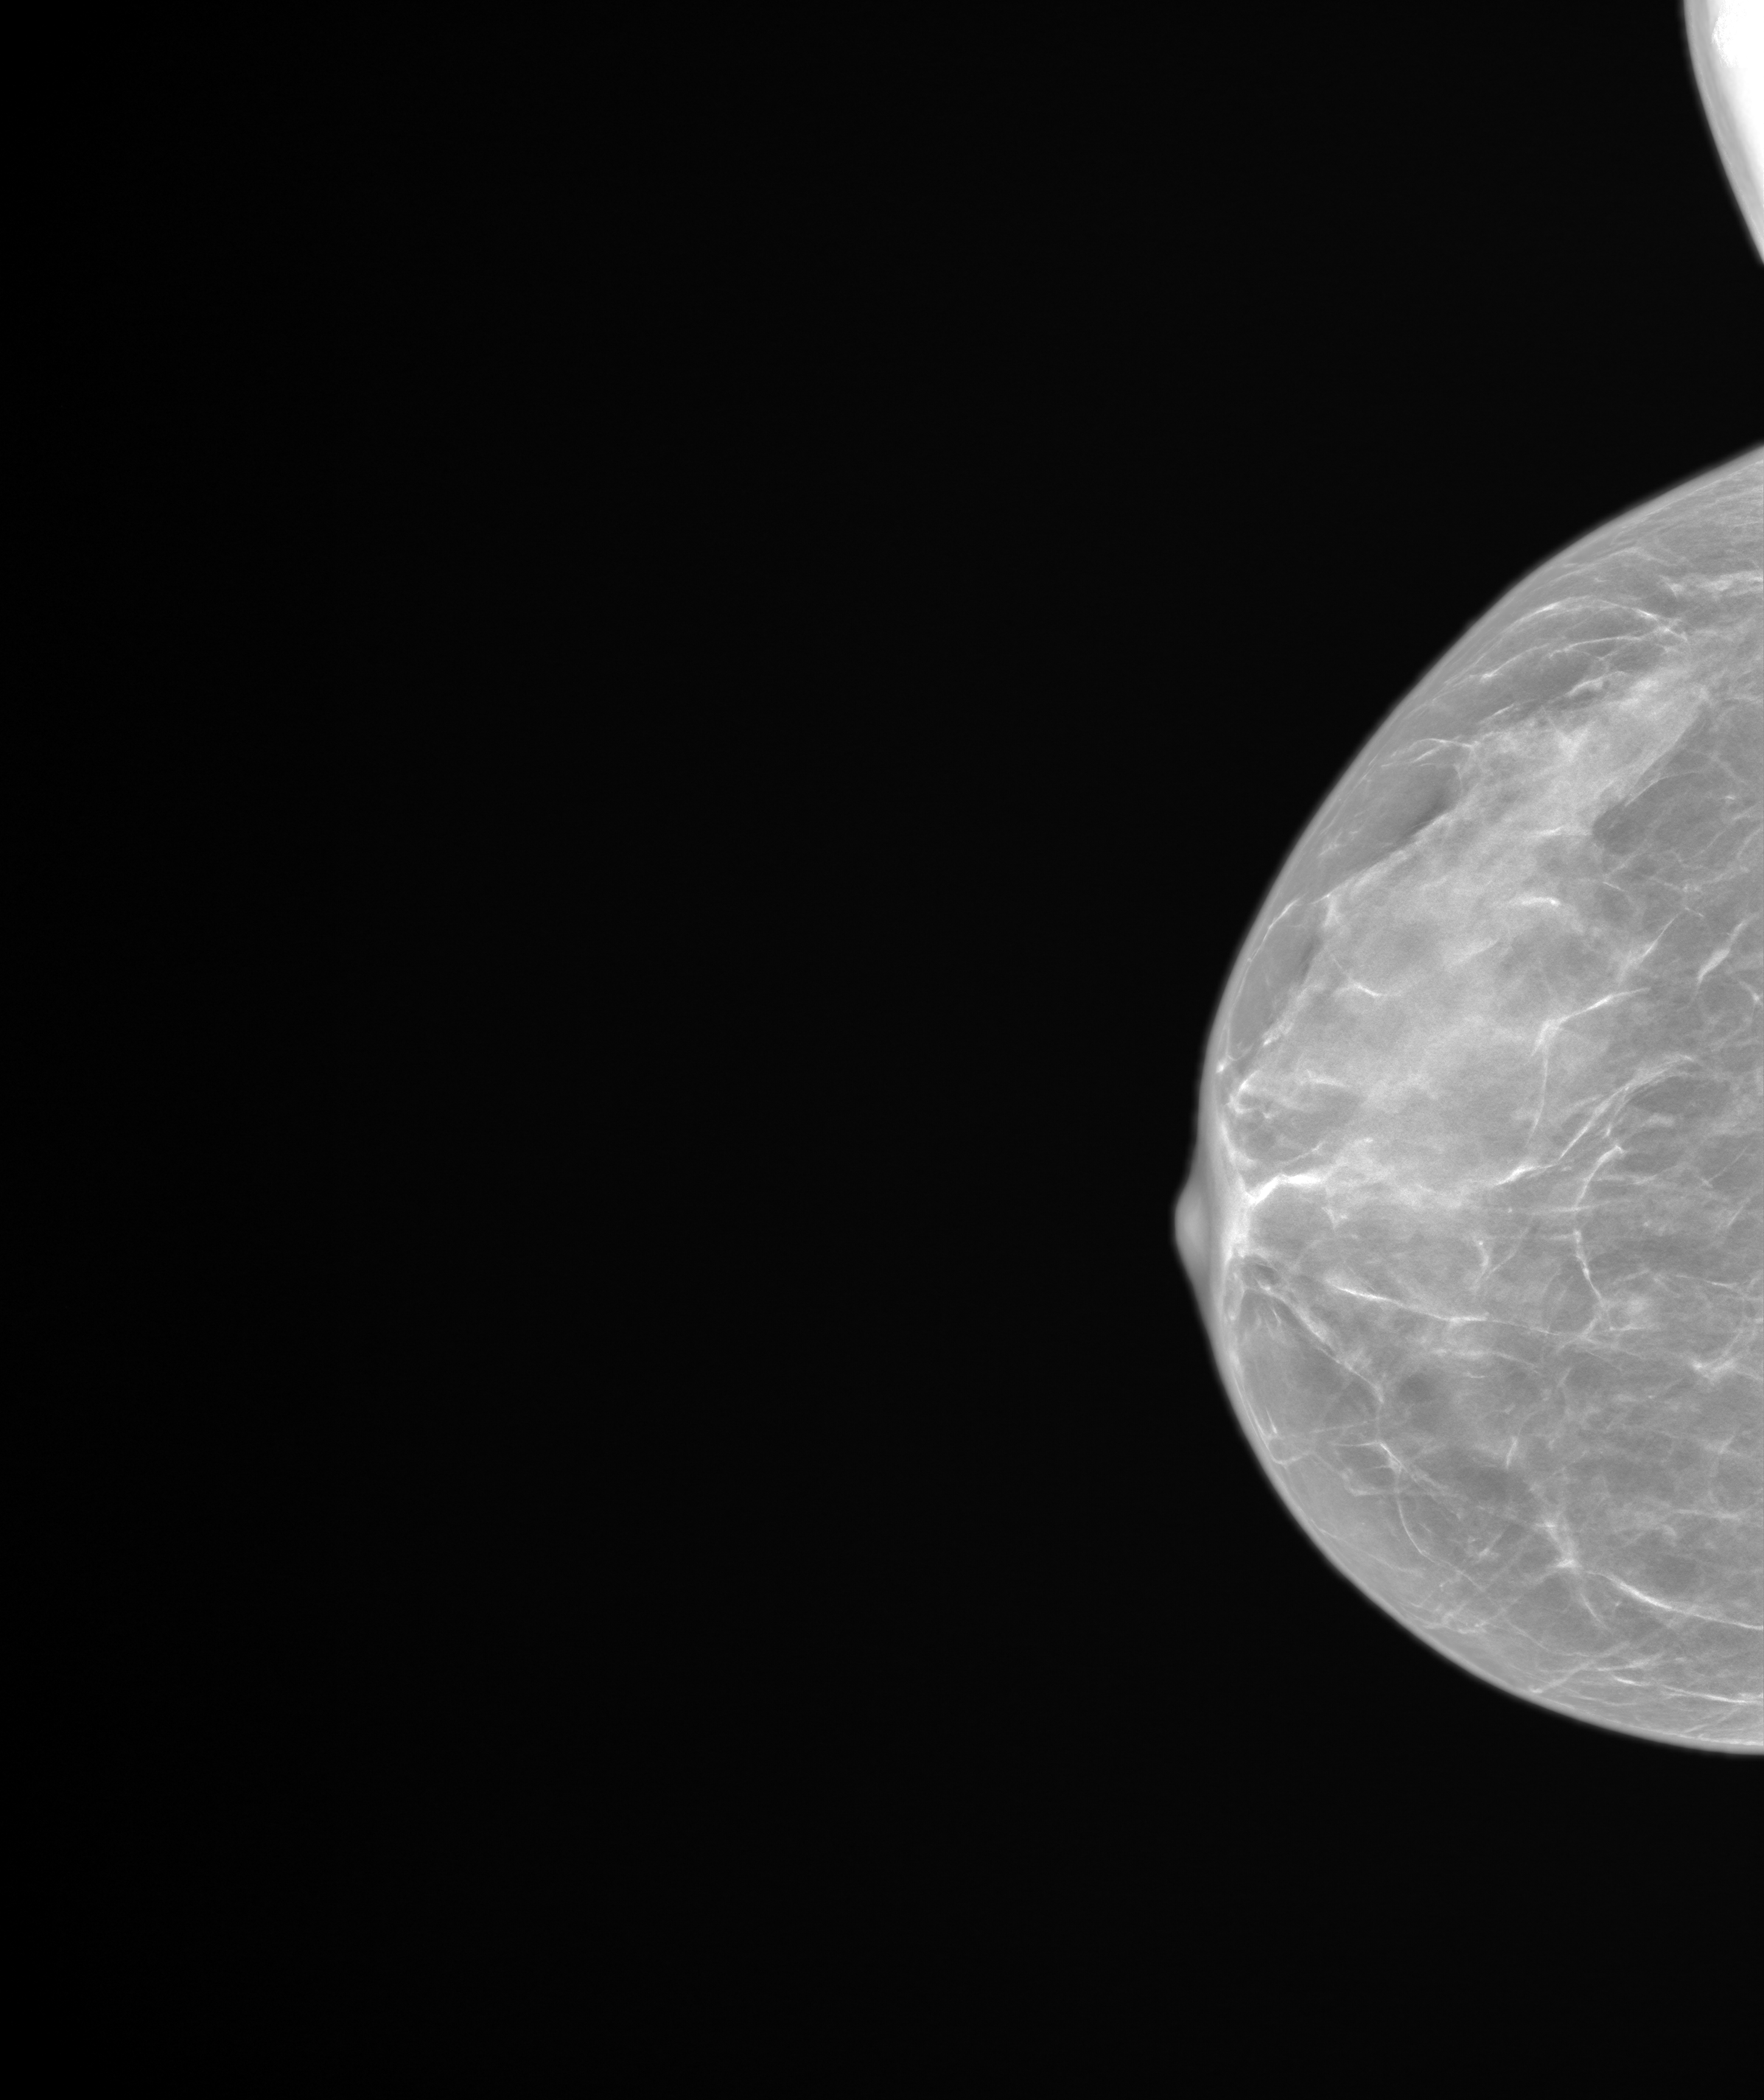
Screening examination. Patient: female, 47 years.
Image type: synthesized 2-D view from tomosynthesis. Breast: right. Projection: CC view. Breast density at the screening exam (both breasts): heterogeneously dense (BI-RADS density category c). Final BI-RADS assessment for this screening round (tomosynthesis exam, both breasts): category 2. Recall: no recall after this screen.